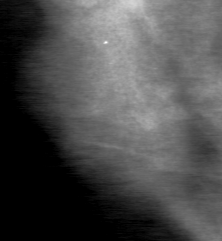
Crop from a digitized film mammogram around one marked abnormality, right breast, CC view, BI-RADS breast density category 4 (scale 1–4).
Marked abnormality: mass, shape lobulated, margins obscured; BI-RADS assessment category 0; subtlety rating 3 on a 1 (subtle) to 5 (obvious) scale; pathology result (as recorded, not read from the image): benign.